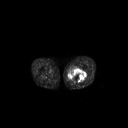
FDG PET of an extremity soft-tissue mass (from a PET/CT study), one axial slice; position 242 of 267 along the scan axis; 3.27 mm slice thickness; 128 × 128 image matrix. Patient: male, 44 years. Case-level facts recorded for this patient, not image findings: histological type: undifferentiated pleomorphic liposarcoma; grade: high; site of the primary tumour: left thigh.
Outlined on this slice (expert contour drawn on MRI and transferred to this co-registered scan by the dataset authors):
- gross tumour volume including surrounding oedema: bounding box (x1, y1, x2, y2) in pixels: (67, 69, 86, 83)
- gross tumour volume (mass): (68, 69, 86, 82)